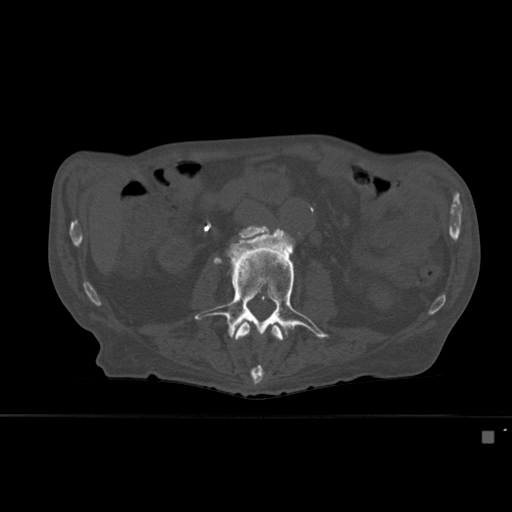
CT including the spine, one axial slice. Slice 216 of 527 in the series (ordered by position). Bone window (W 1800 / L 400 HU). 1.5 mm slice thickness. 512 × 512 image matrix, field of view 373 × 373 mm. Patient: male, 78 years. From the clinical record (not read from this slice): primary cancer: prostate.
Annotated regions visible in this slice (semi-automatic segmentation, software-assisted and operator-edited):
- L2 vertebra: bounding box <233,320,284,385> (left, top, right, bottom; pixels)
- L3 vertebra: <194,228,329,339>
- L4 vertebra: <240,227,267,238>